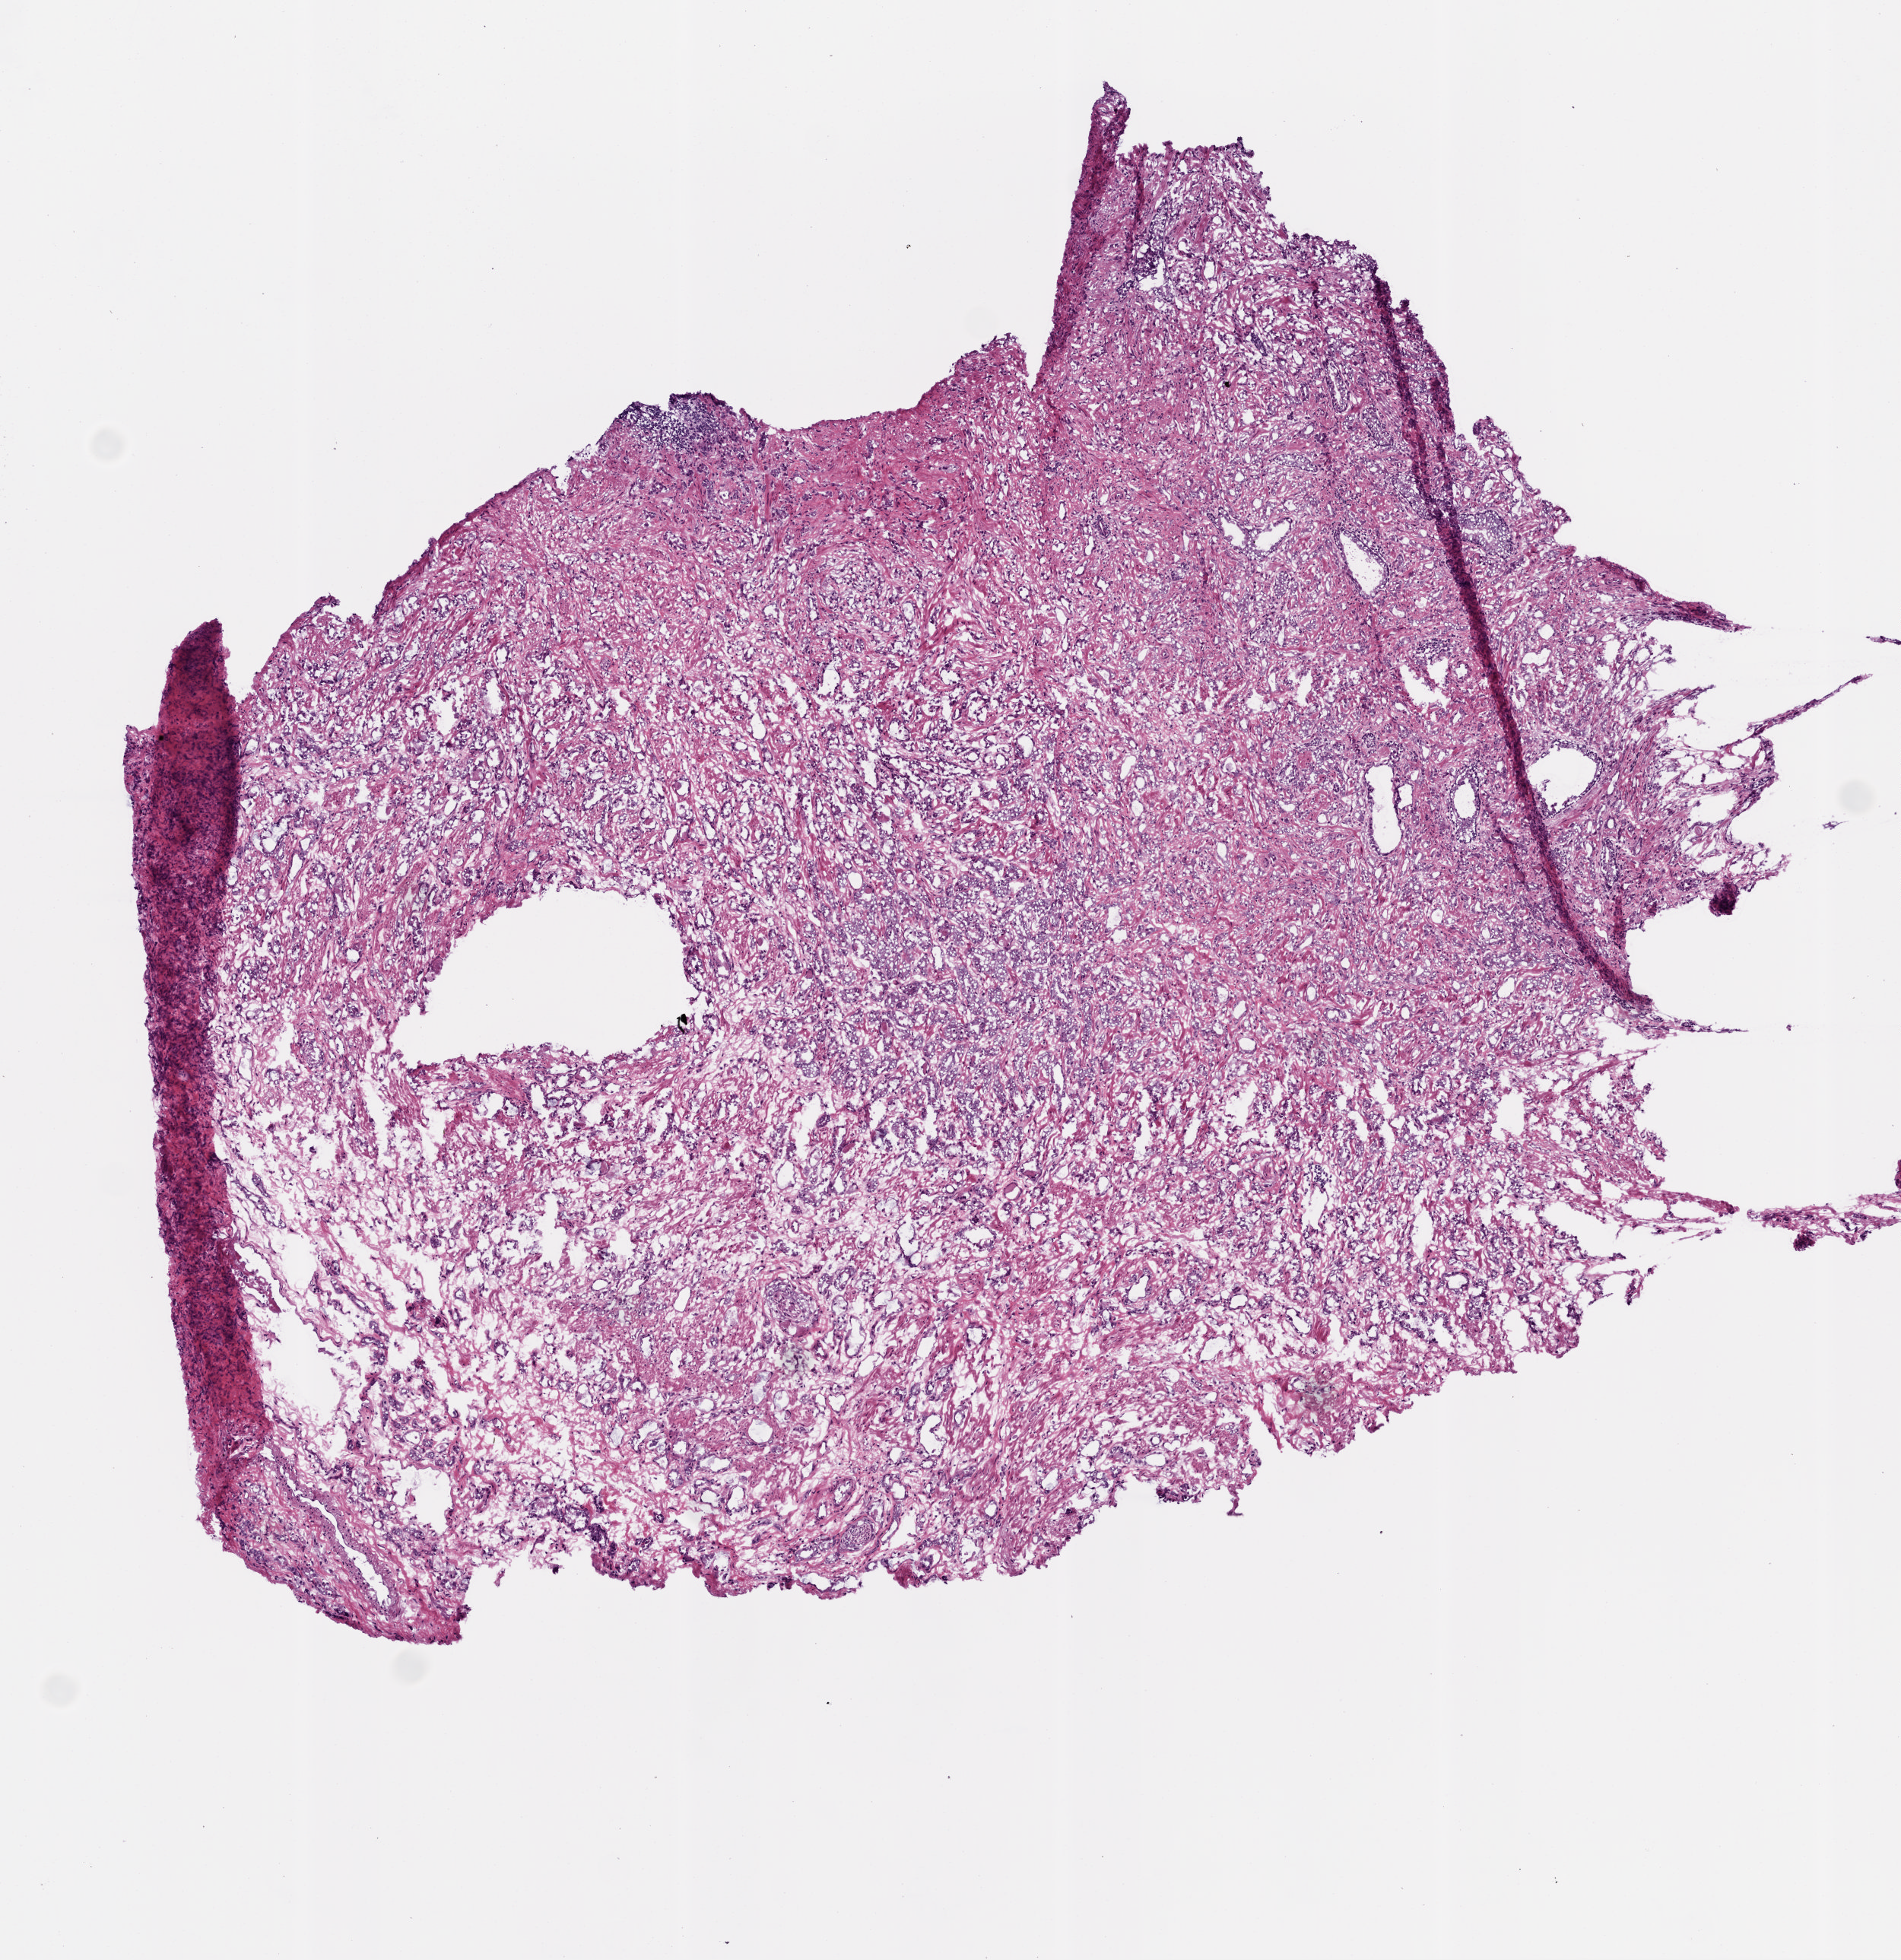
Whole-slide histology image, H&E-stained — low-resolution overview of the scanned area, about 5.0 x 5.2 mm (from a 20x scan). Frozen section. Primary tumour sample from the prostate. Patient: male, age at initial diagnosis 68 years.
Histologic diagnosis: Acinar cell carcinoma (prostate gland).